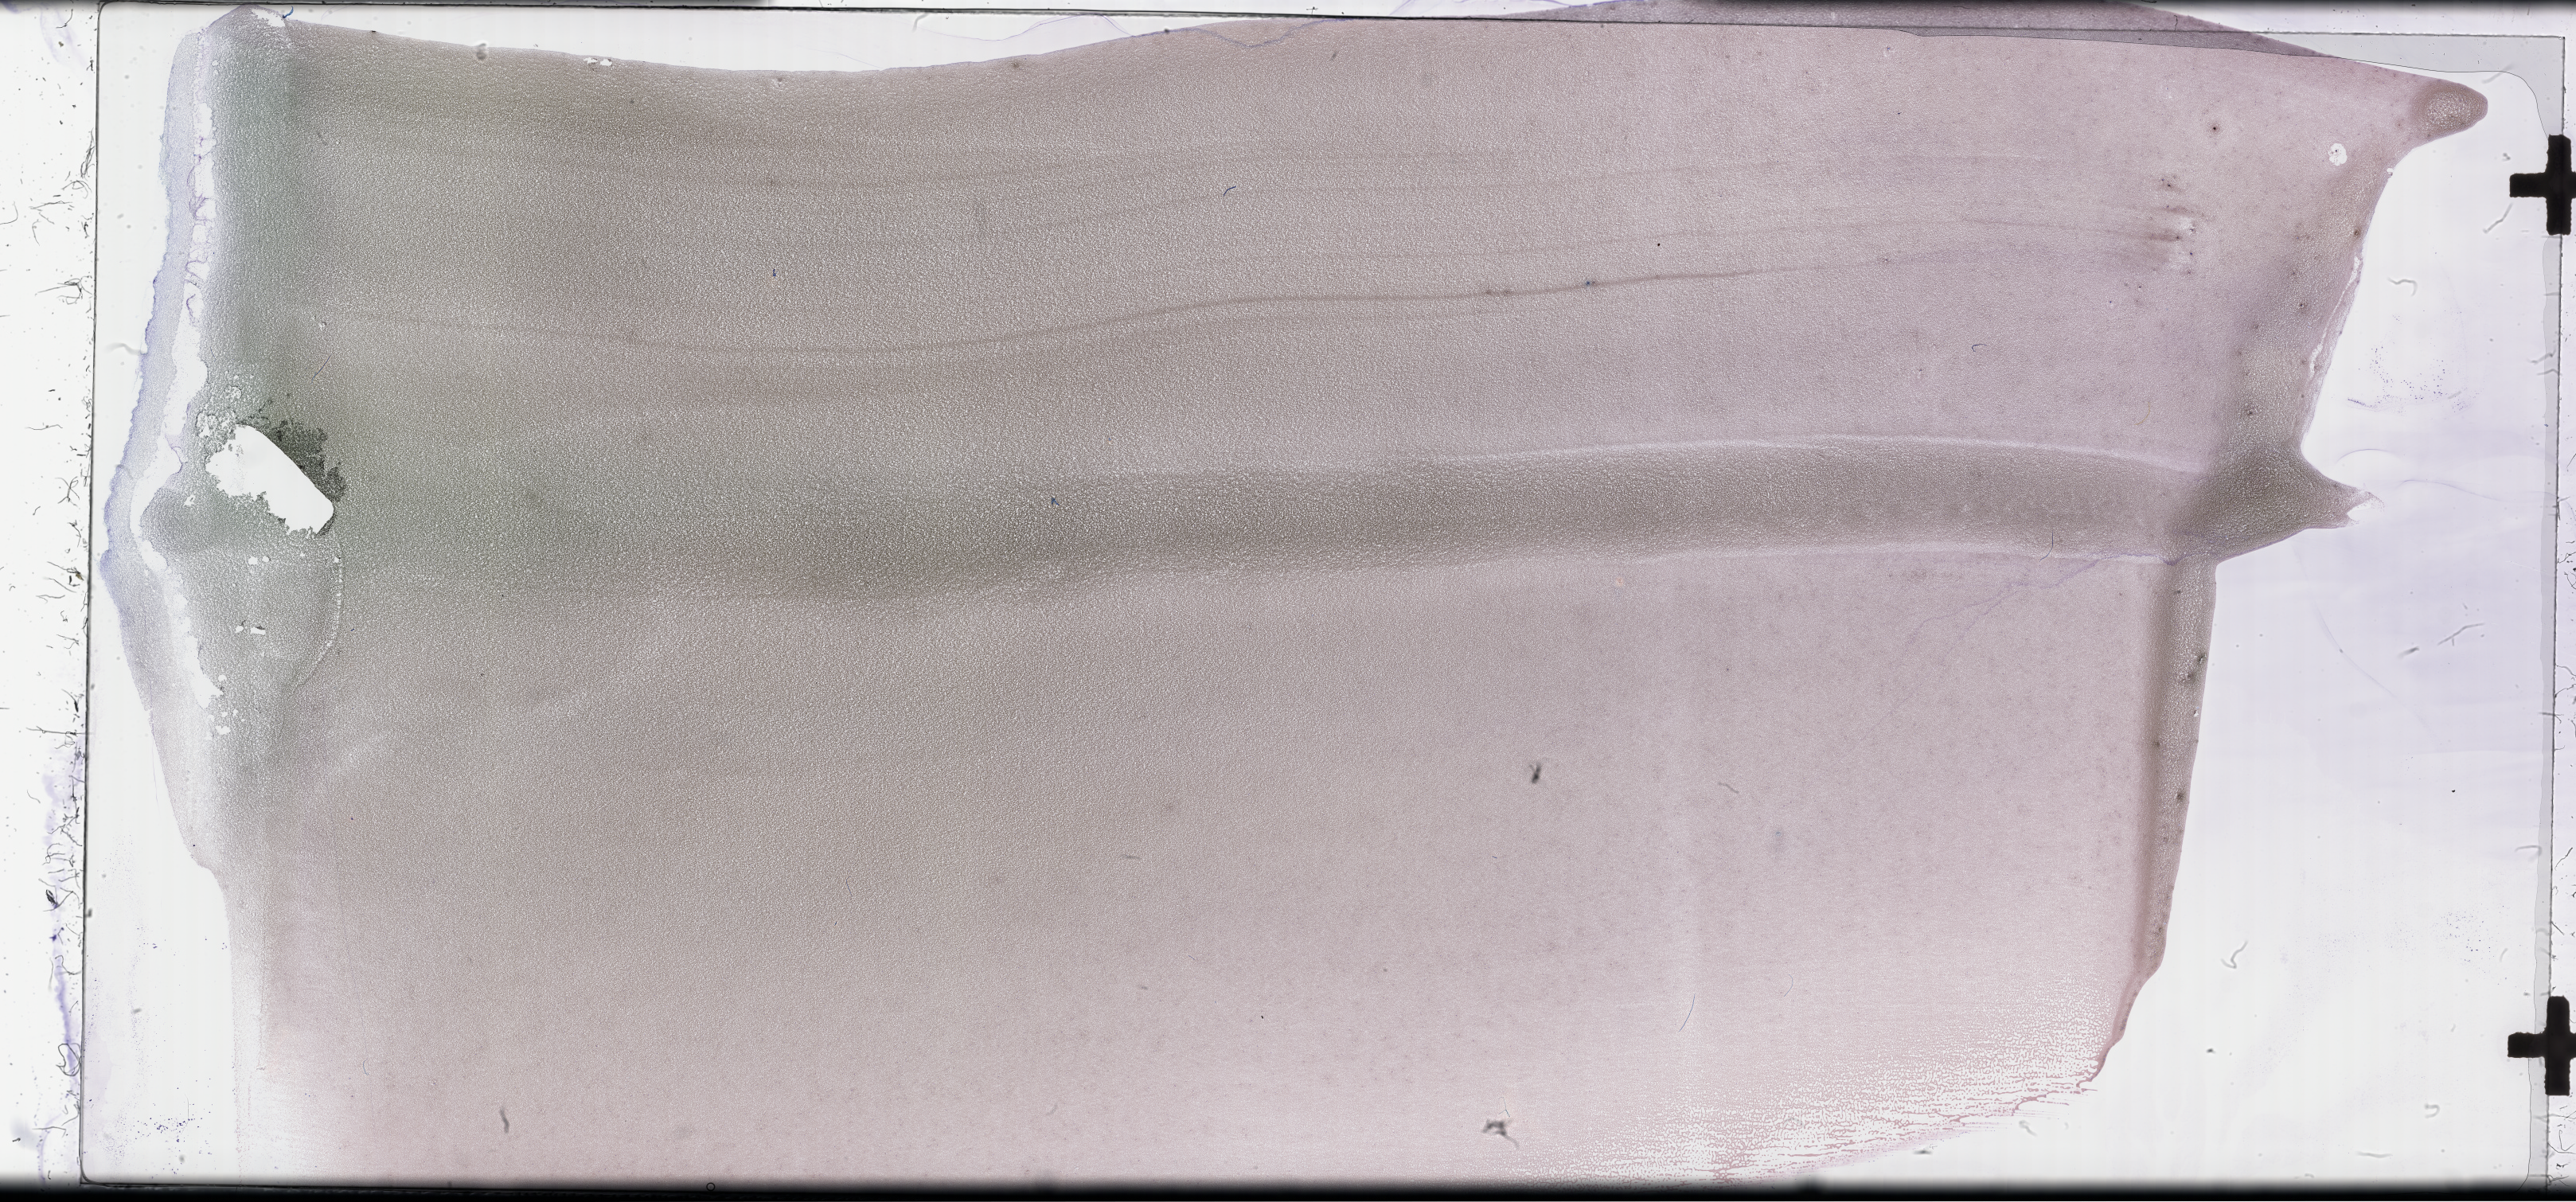
Whole-slide image of a whole blood smear, Wright–Giemsa stain — a low-resolution overview of the entire scanned area, about 52.3 x 24.4 mm. Specimen time point: collected on treatment. Patient sex: male.
- from a patient with: Plasma Cell Myeloma